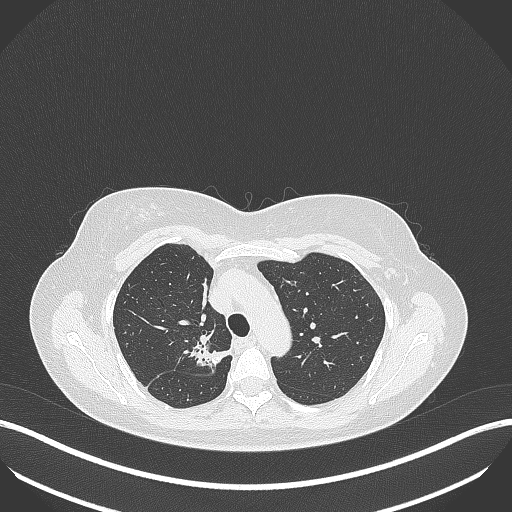
Chest CT, one axial slice; position 290 of 386 along the scan axis; reconstruction kernel B70f; lung window (W 1500 / L -600 HU); 1 mm slice thickness; 512 × 512 image matrix, field of view 400 × 400 mm. Female patient, age 65 years. From the clinical record (not read from this slice): clinical TNM (as recorded): T1b N0 M0; histopathological grade: G2.
Structures marked on this image (bounding box drawn by a radiologist):
- lung tumour (recorded histology: adenocarcinoma): bounding box [x1, y1, x2, y2] px = [185, 340, 230, 374]